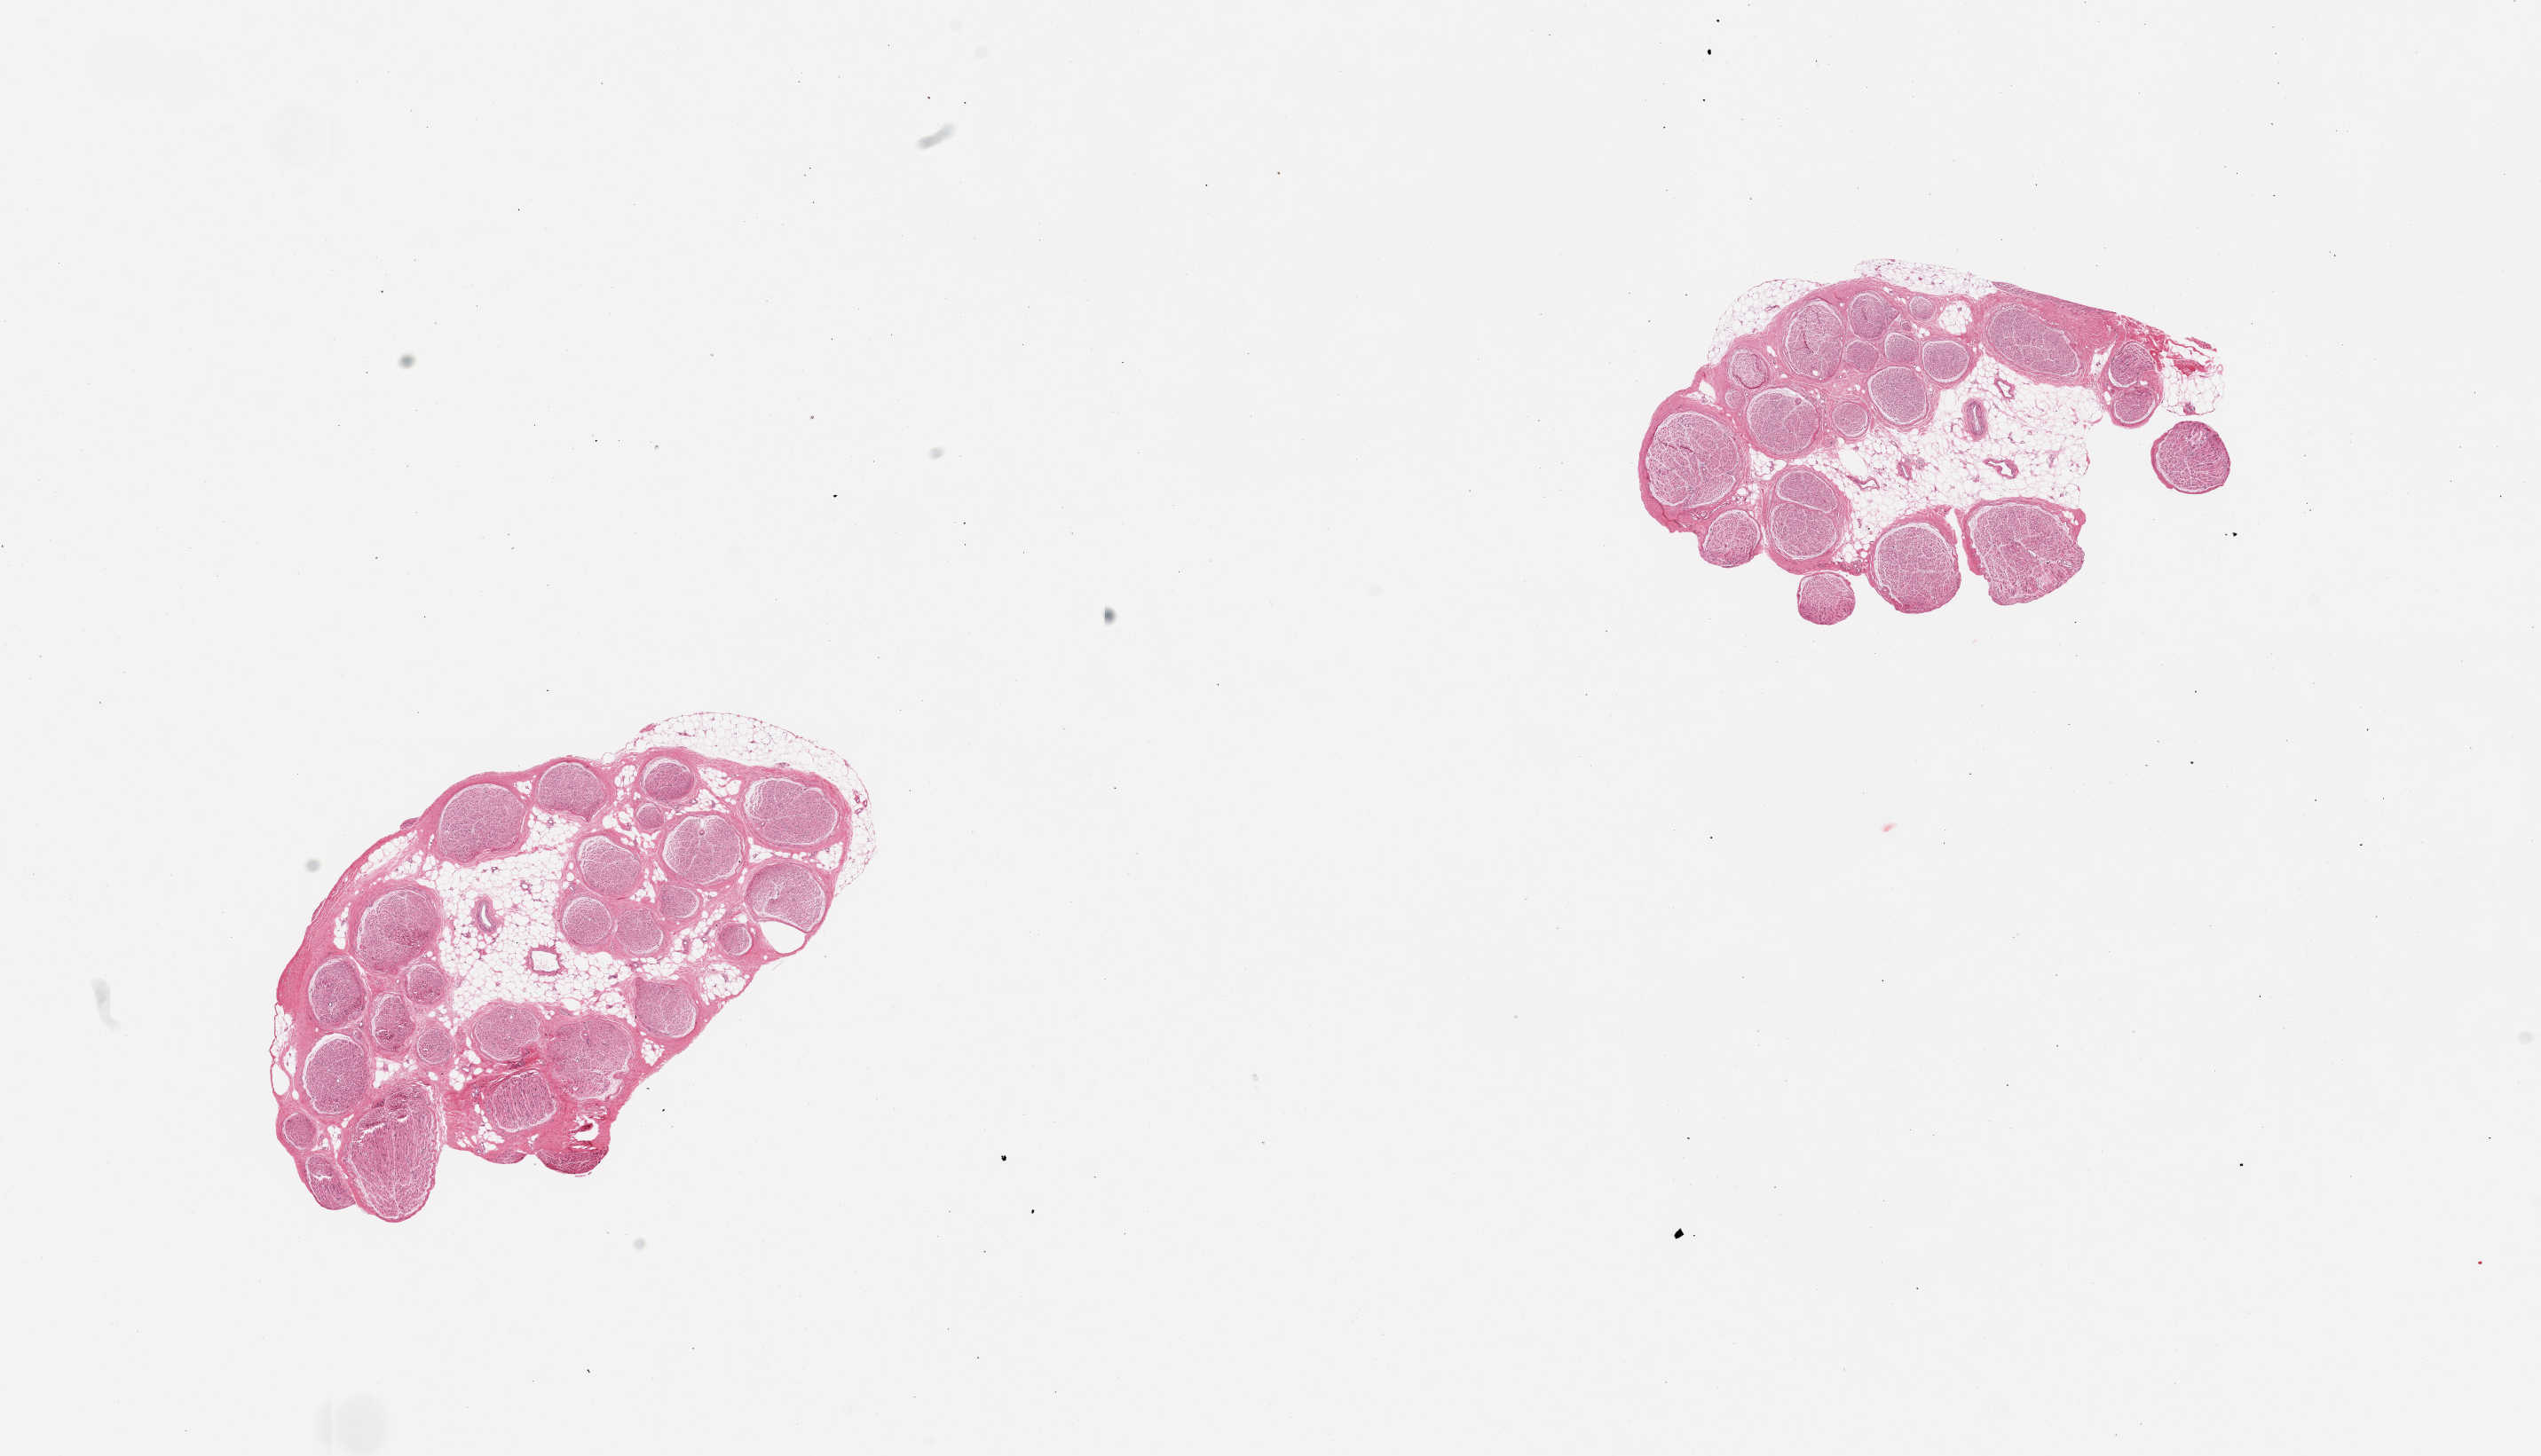
Whole-slide image, hematoxylin and eosin (H&E) stain, brightfield, low-resolution overview of the scanned area, about 22.6 x 13.0 mm, PAXgene-fixed paraffin-embedded (PFPE) section, target tissue: tibial nerve, tissue donor sample. Female donor.
Review note (as recorded): 2 pieces; 40 & 20% internal fat.